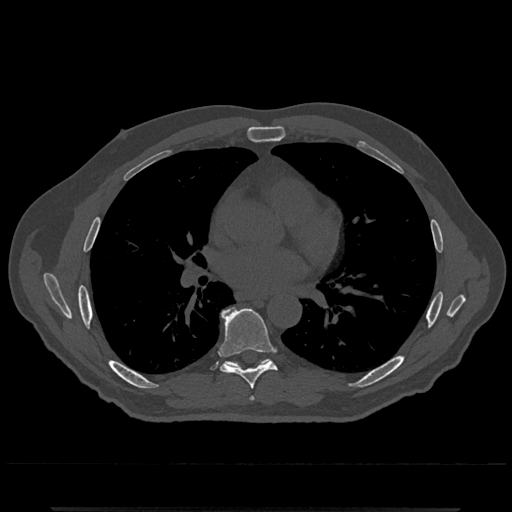
CT including the spine, one axial slice; position 712 of 797 along the scan axis; 120 kVp; bone window (W 1800 / L 400 HU); 0.5 mm slice thickness; 512 × 512 image matrix, field of view 393 × 393 mm. Male patient, age 67 years. From the clinical record (not read from this slice): primary cancer: prostate.
Structures marked on this image (semi-automatically segmented with operator editing):
- T6 vertebra: bounding box [x1, y1, x2, y2] px = [251, 397, 254, 400]
- T7 vertebra: [219, 308, 276, 390]
- T8 vertebra: [221, 308, 270, 367]